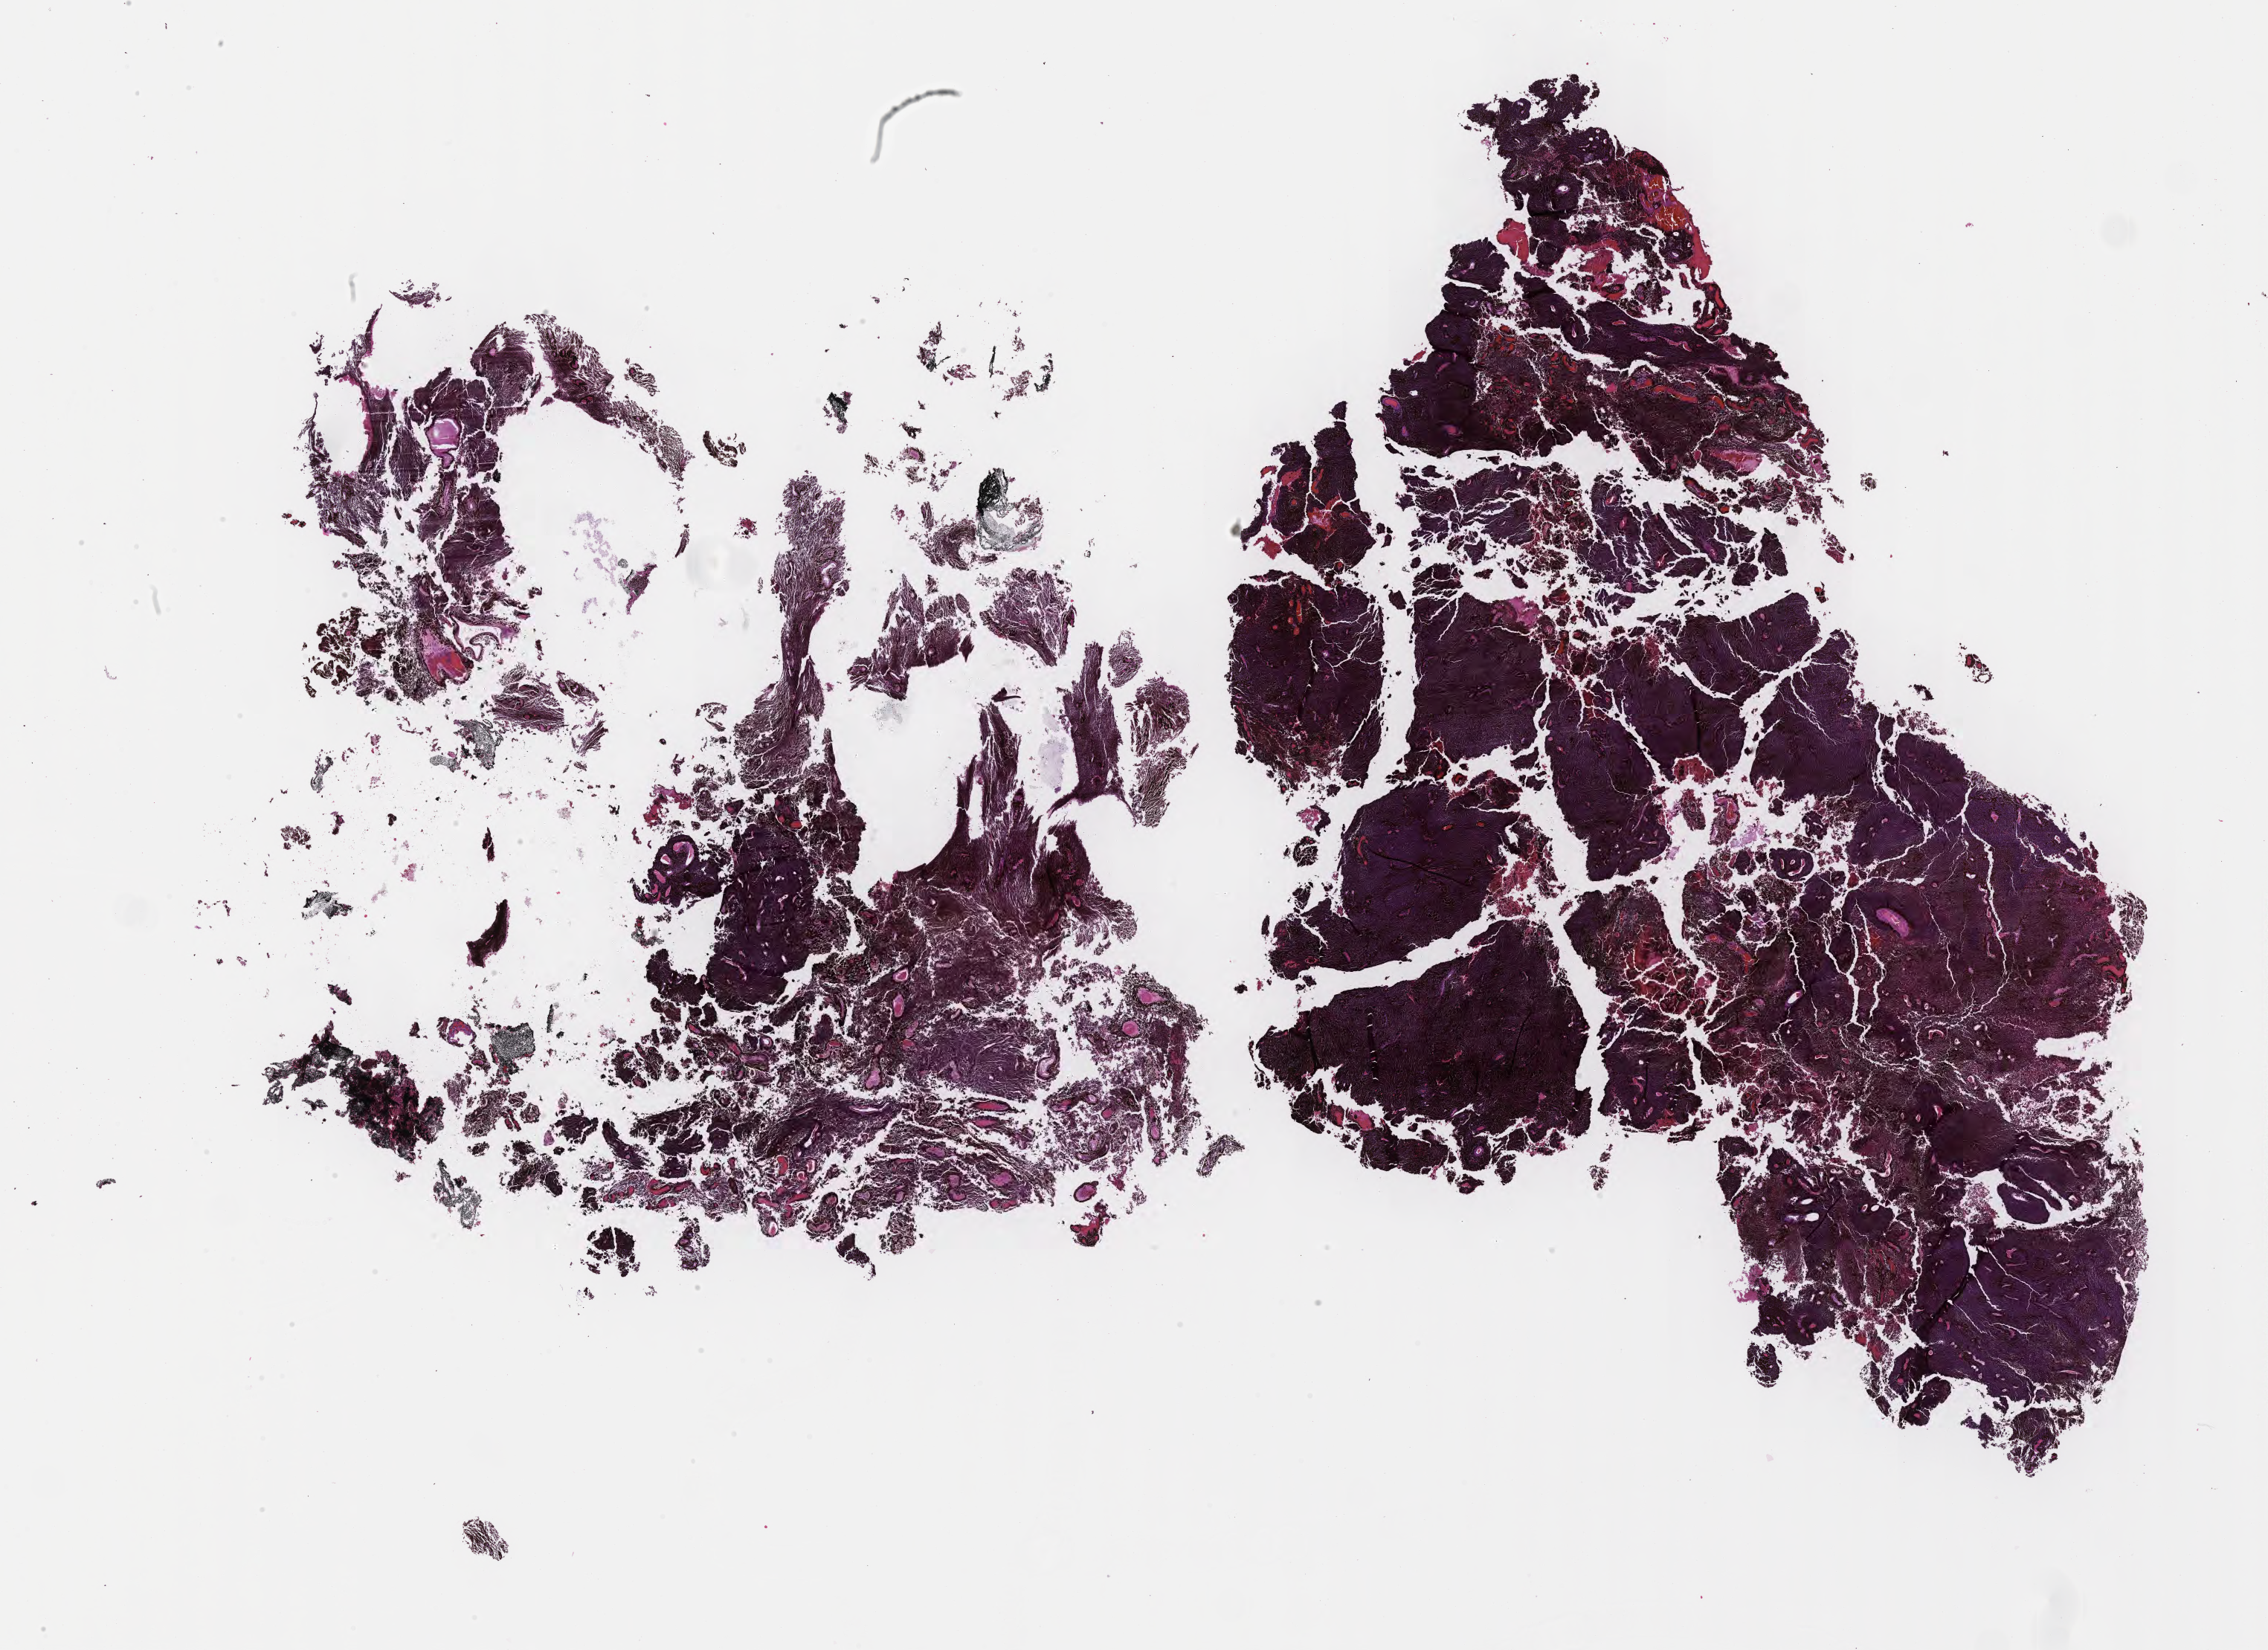
Whole-slide image, H&E stain of tumor tissue from the brain, whole scanned area (about 24.7 x 17.9 mm) shown as a low-resolution overview, formalin-fixed paraffin-embedded section. Patient female; age 245 months (20 years 5 months).
Recorded diagnosis: Meningeal melanocytoma.